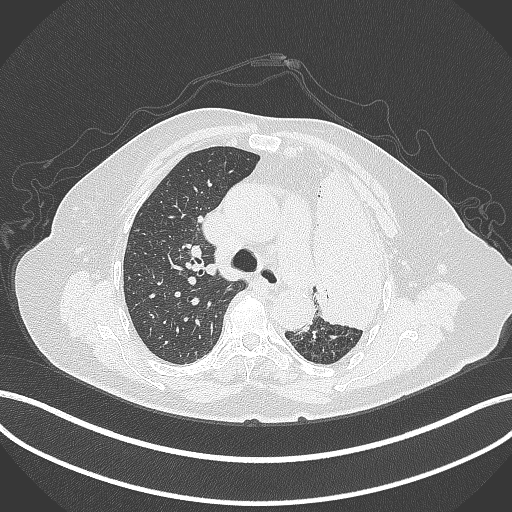
Chest CT, one axial slice; position 267 of 399 along the scan axis; reconstruction kernel B70f; 120 kVp; lung window (W 1500 / L -600 HU); 1 mm slice thickness; 512 × 512 image matrix, field of view 400 × 400 mm. Female patient, age 75 years. Case-level facts recorded for this patient, not image findings: clinical TNM (as recorded): T3 N3 M1.
Structures marked on this image (bounding box drawn by a radiologist):
- lung tumour (recorded histology: adenocarcinoma): bounding box <311,164,395,332> (left, top, right, bottom; pixels)